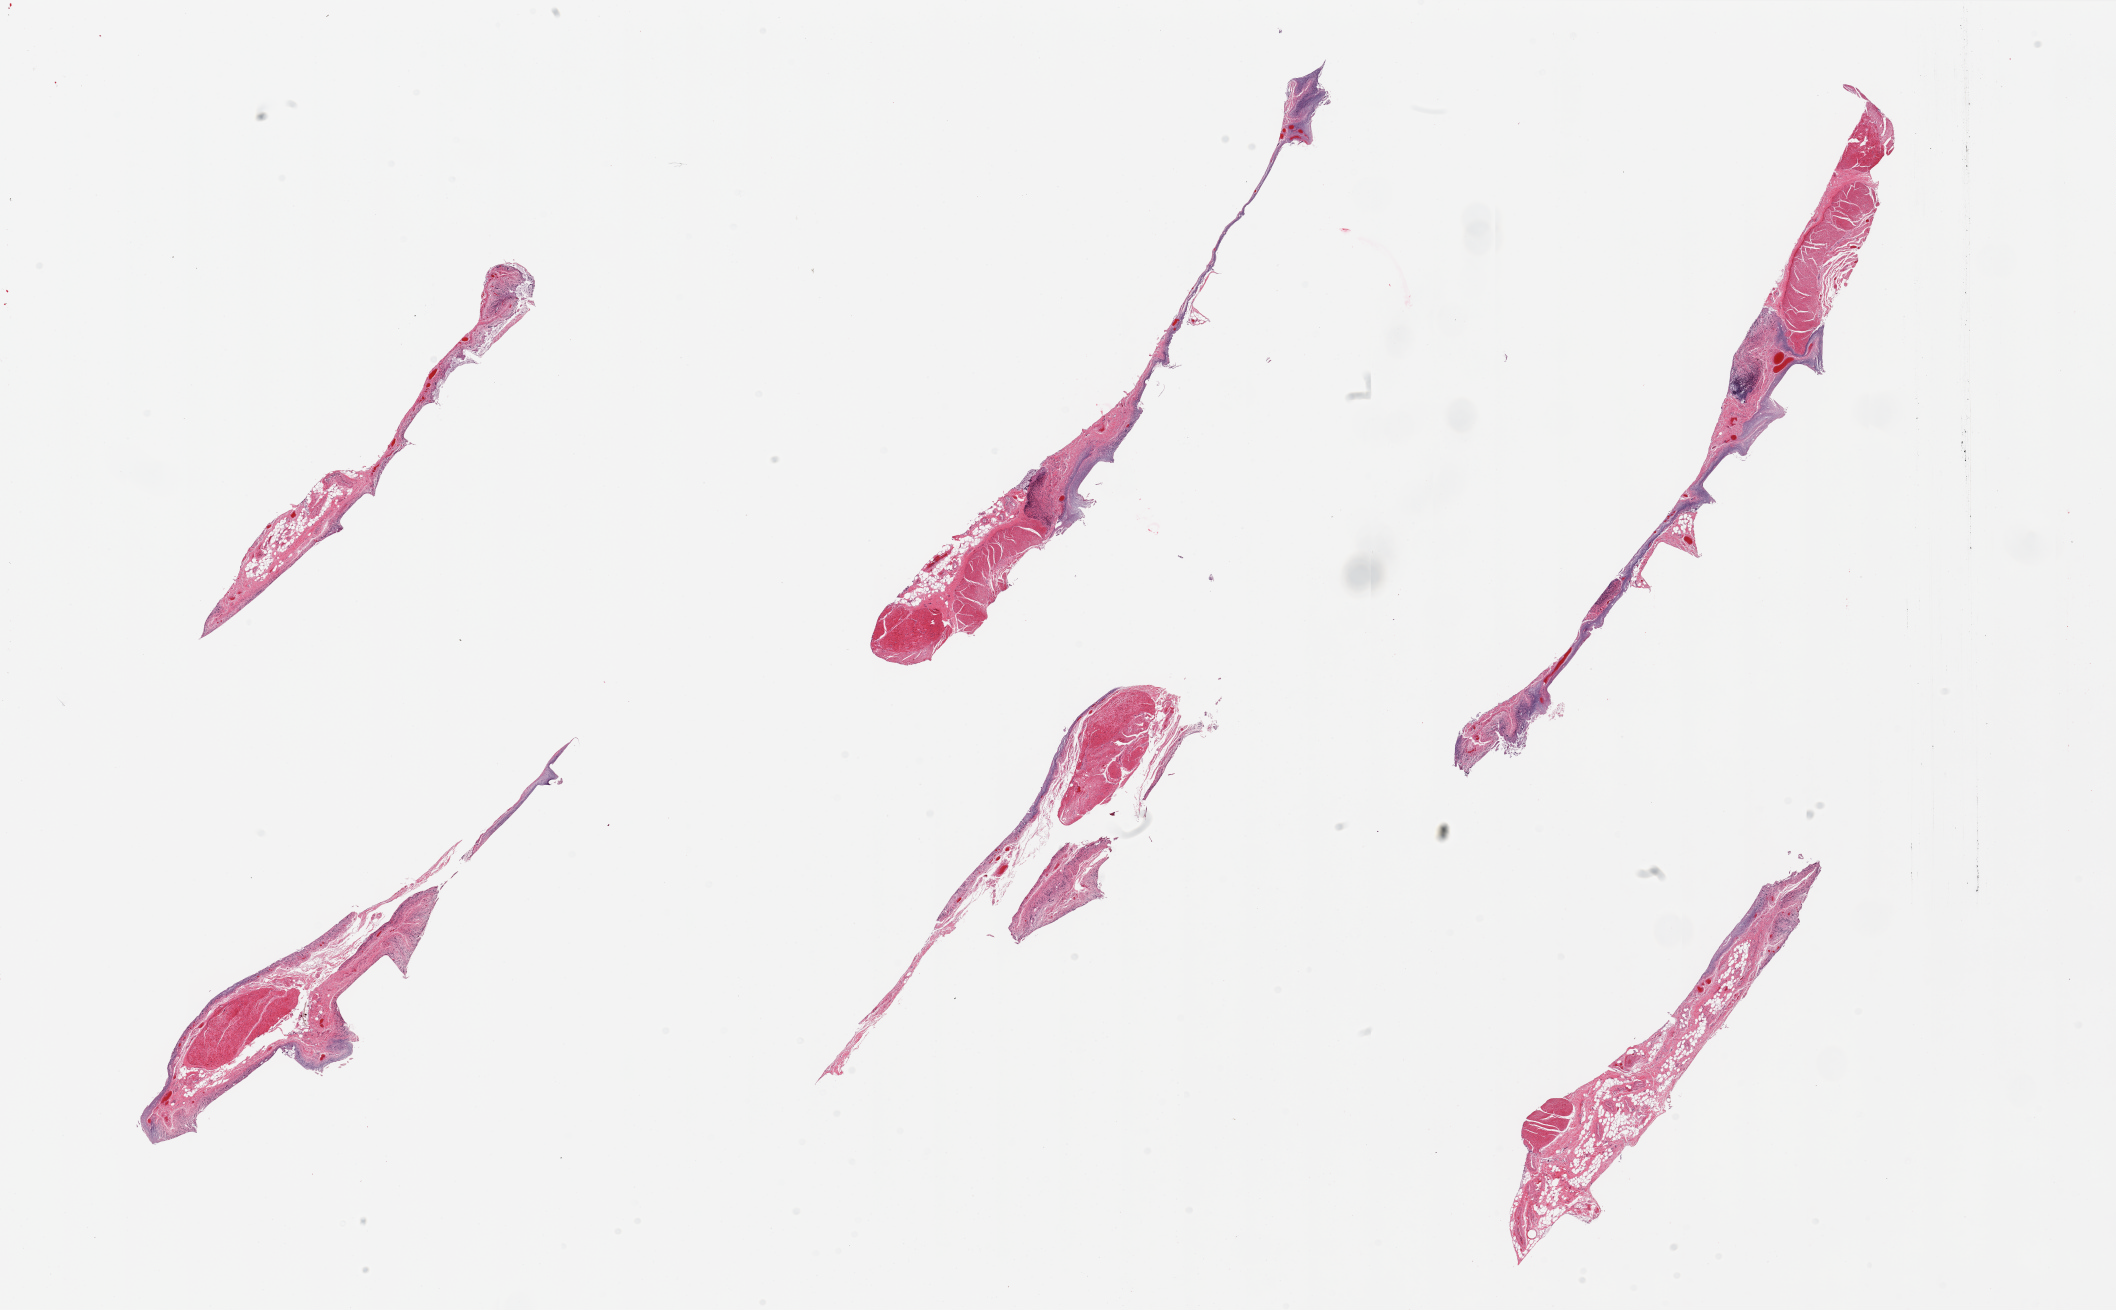
Hematoxylin and eosin (H&E) whole-slide image, brightfield — a low-resolution overview of the entire scanned area, about 33.5 x 20.7 mm; PAXgene-fixed paraffin-embedded (PFPE) section; sampled site (target tissue): transverse colon; tissue donor sample. Male donor.
- reviewer comment on this tissue sample: 6 pieces; autolyzed mucosa, residual muscularis